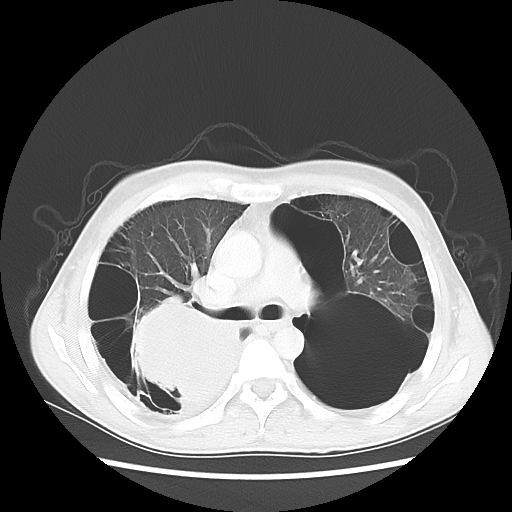
Chest CT, one axial slice; position 35 of 57 along the scan axis; reconstruction kernel LUNG; lung window (W 1500 / L -600 HU); 5 mm slice thickness; 512 × 512 image matrix, field of view 351 × 351 mm. Patient: male, 41 years. From the clinical record (not read from this slice): clinical TNM (as recorded): T4 N0 M1a; histopathological grade: G3.
Annotated regions visible in this slice (bounding box drawn by a radiologist):
- lung tumour (recorded histology: large cell carcinoma): bounding box [x1, y1, x2, y2] px = [127, 298, 250, 416]